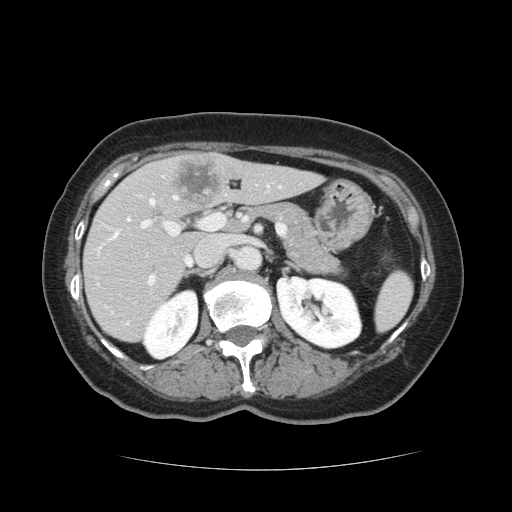
Contrast-enhanced abdominal CT, one axial slice. Position 66 of 128 along the scan axis. 120 kVp. Intravenous contrast given. Soft-tissue window (W 400 / L 40 HU). 512 × 512 image matrix. Female patient, age 67 years. From the clinical record (not read from this slice): diagnosis: colorectal cancer liver metastases, imaged before liver resection; multiple liver metastases: yes; largest metastasis: 3 cm.
Annotated regions visible in this slice (expert manual segmentation):
- hepatic veins: box from (x=113, y=196) to (x=191, y=264) px
- liver: (x=84, y=153)–(x=320, y=342)
- planned liver remnant (the part of the liver to remain after resection): (x=84, y=163)–(x=320, y=342)
- portal vein (with intrahepatic branches): (x=140, y=182)–(x=274, y=286)
- liver metastasis: (x=173, y=160)–(x=219, y=205)